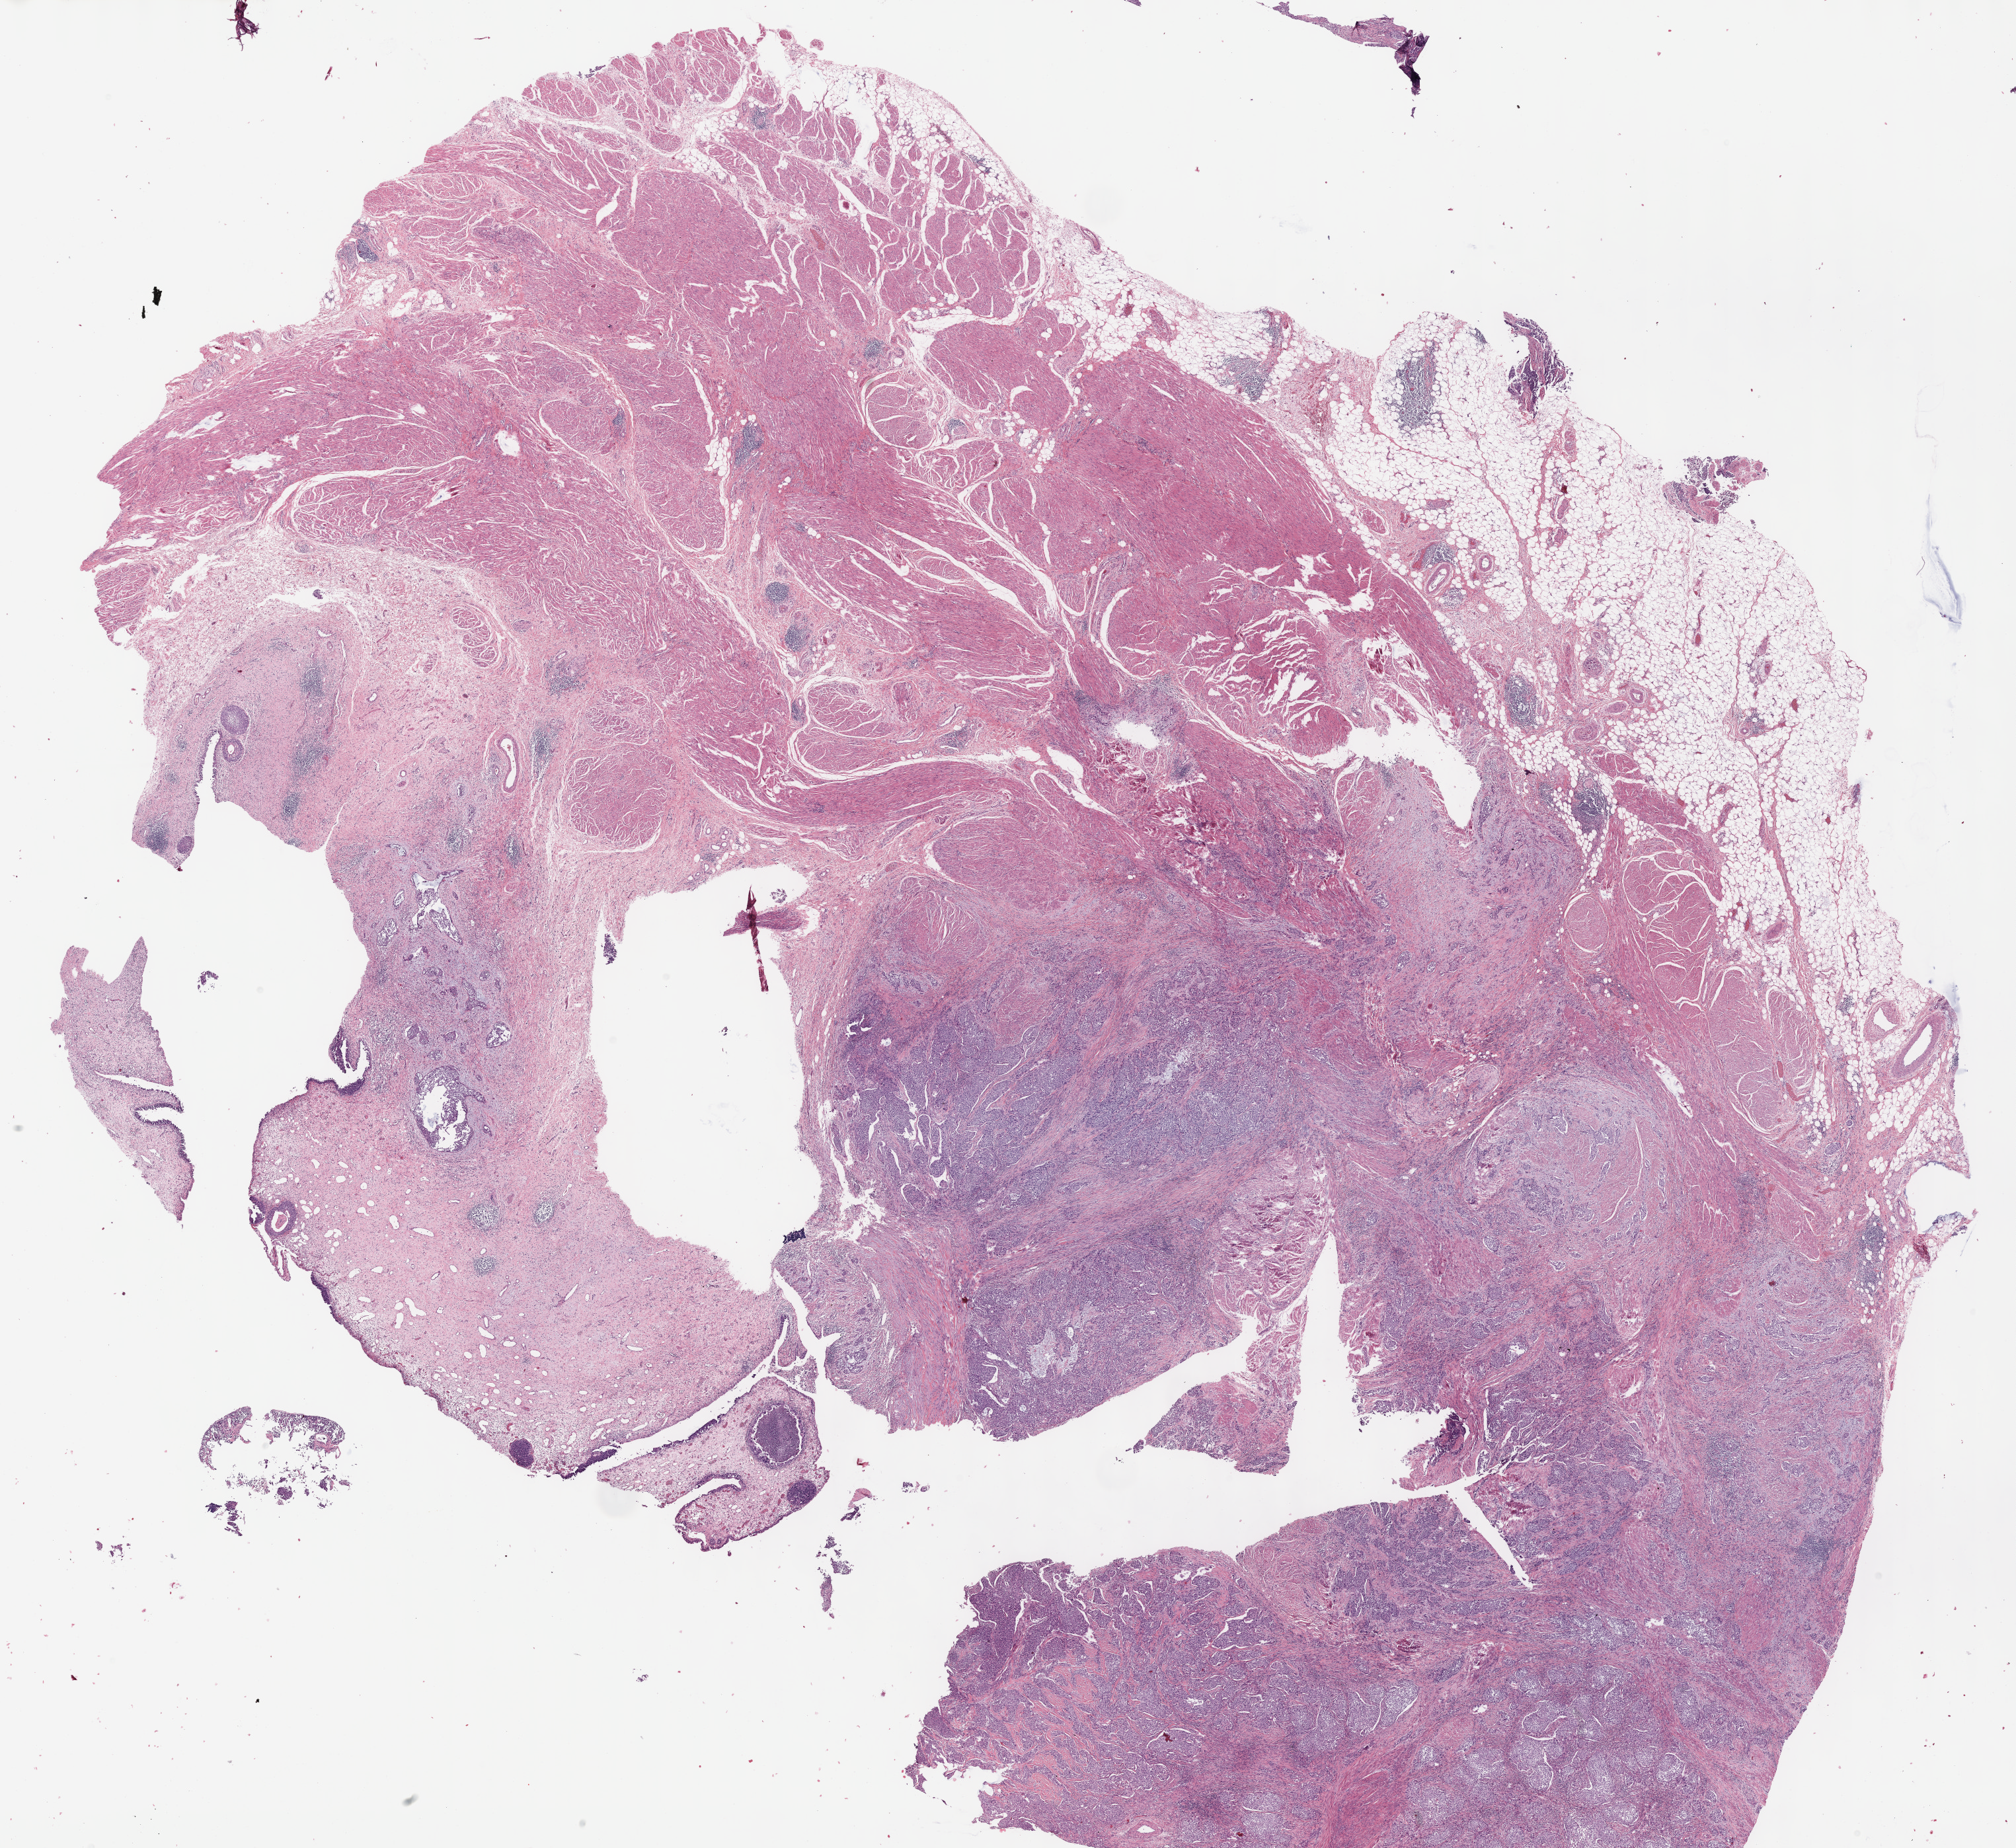
Whole-slide histology image, H&E-stained, a low-resolution overview of the entire scanned area, about 24.6 x 22.6 mm (from a 40x scan), FFPE section, sample: primary tumour, bladder. Patient: male, age at initial diagnosis 59 years. Histologic grade: high grade.
Pathologic diagnosis: Transitional cell carcinoma (posterior wall of bladder). Lymph nodes positive (case pathology): 1 of 19 examined. TNM: T2a N1 M0. AJCC pathologic stage: IV (7th edition).